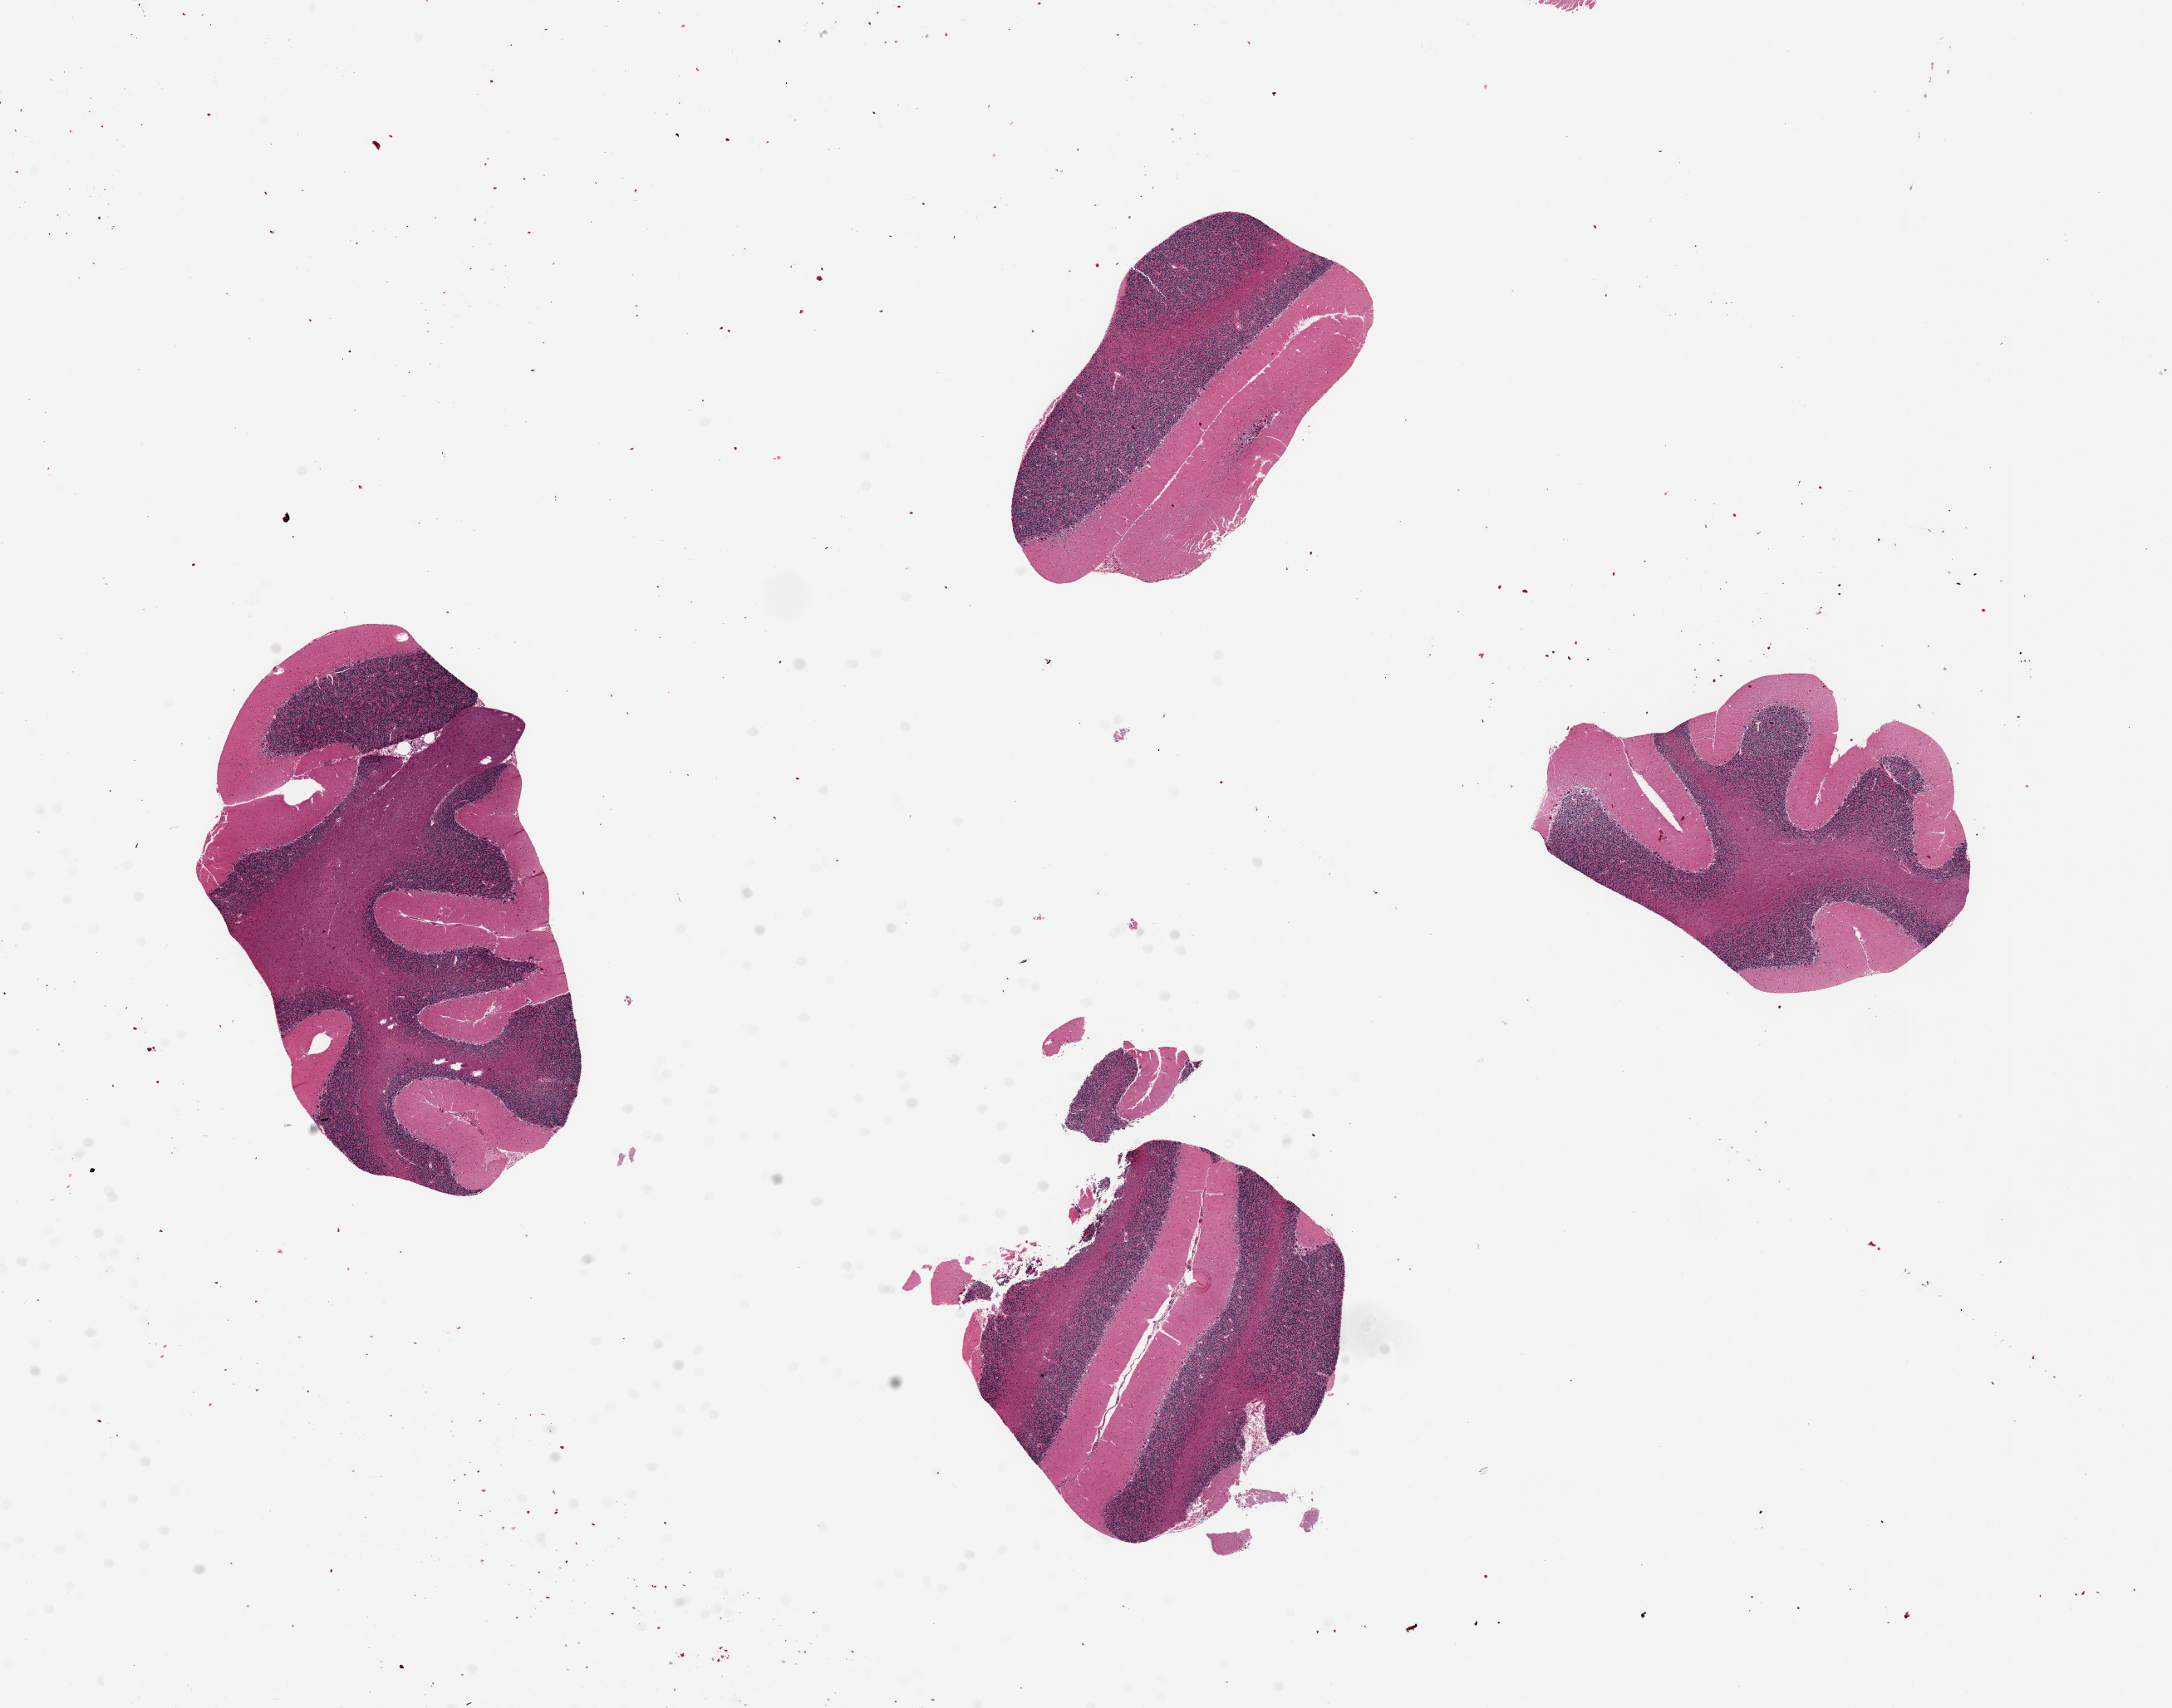
Whole-slide image, hematoxylin and eosin (H&E) stain — low-resolution overview of the scanned area, about 20.7 x 16.3 mm (slide scanned at 20x), PAXgene-fixed, paraffin-embedded tissue, target tissue: cerebellum, donor tissue sample. Donor: male.
Reviewer comment on this tissue sample: 4 pieces ~5x3mm, Purkinje cells show minimal ischemic damage.